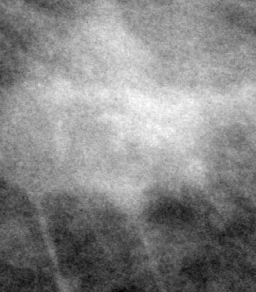
Cropped region of a digitized screen-film mammogram centred on a radiologist-marked abnormality, left breast, MLO view.
Finding: mass, shape irregular / architectural distortion, margins spiculated; BI-RADS assessment category 4; pathology (as recorded): malignant.